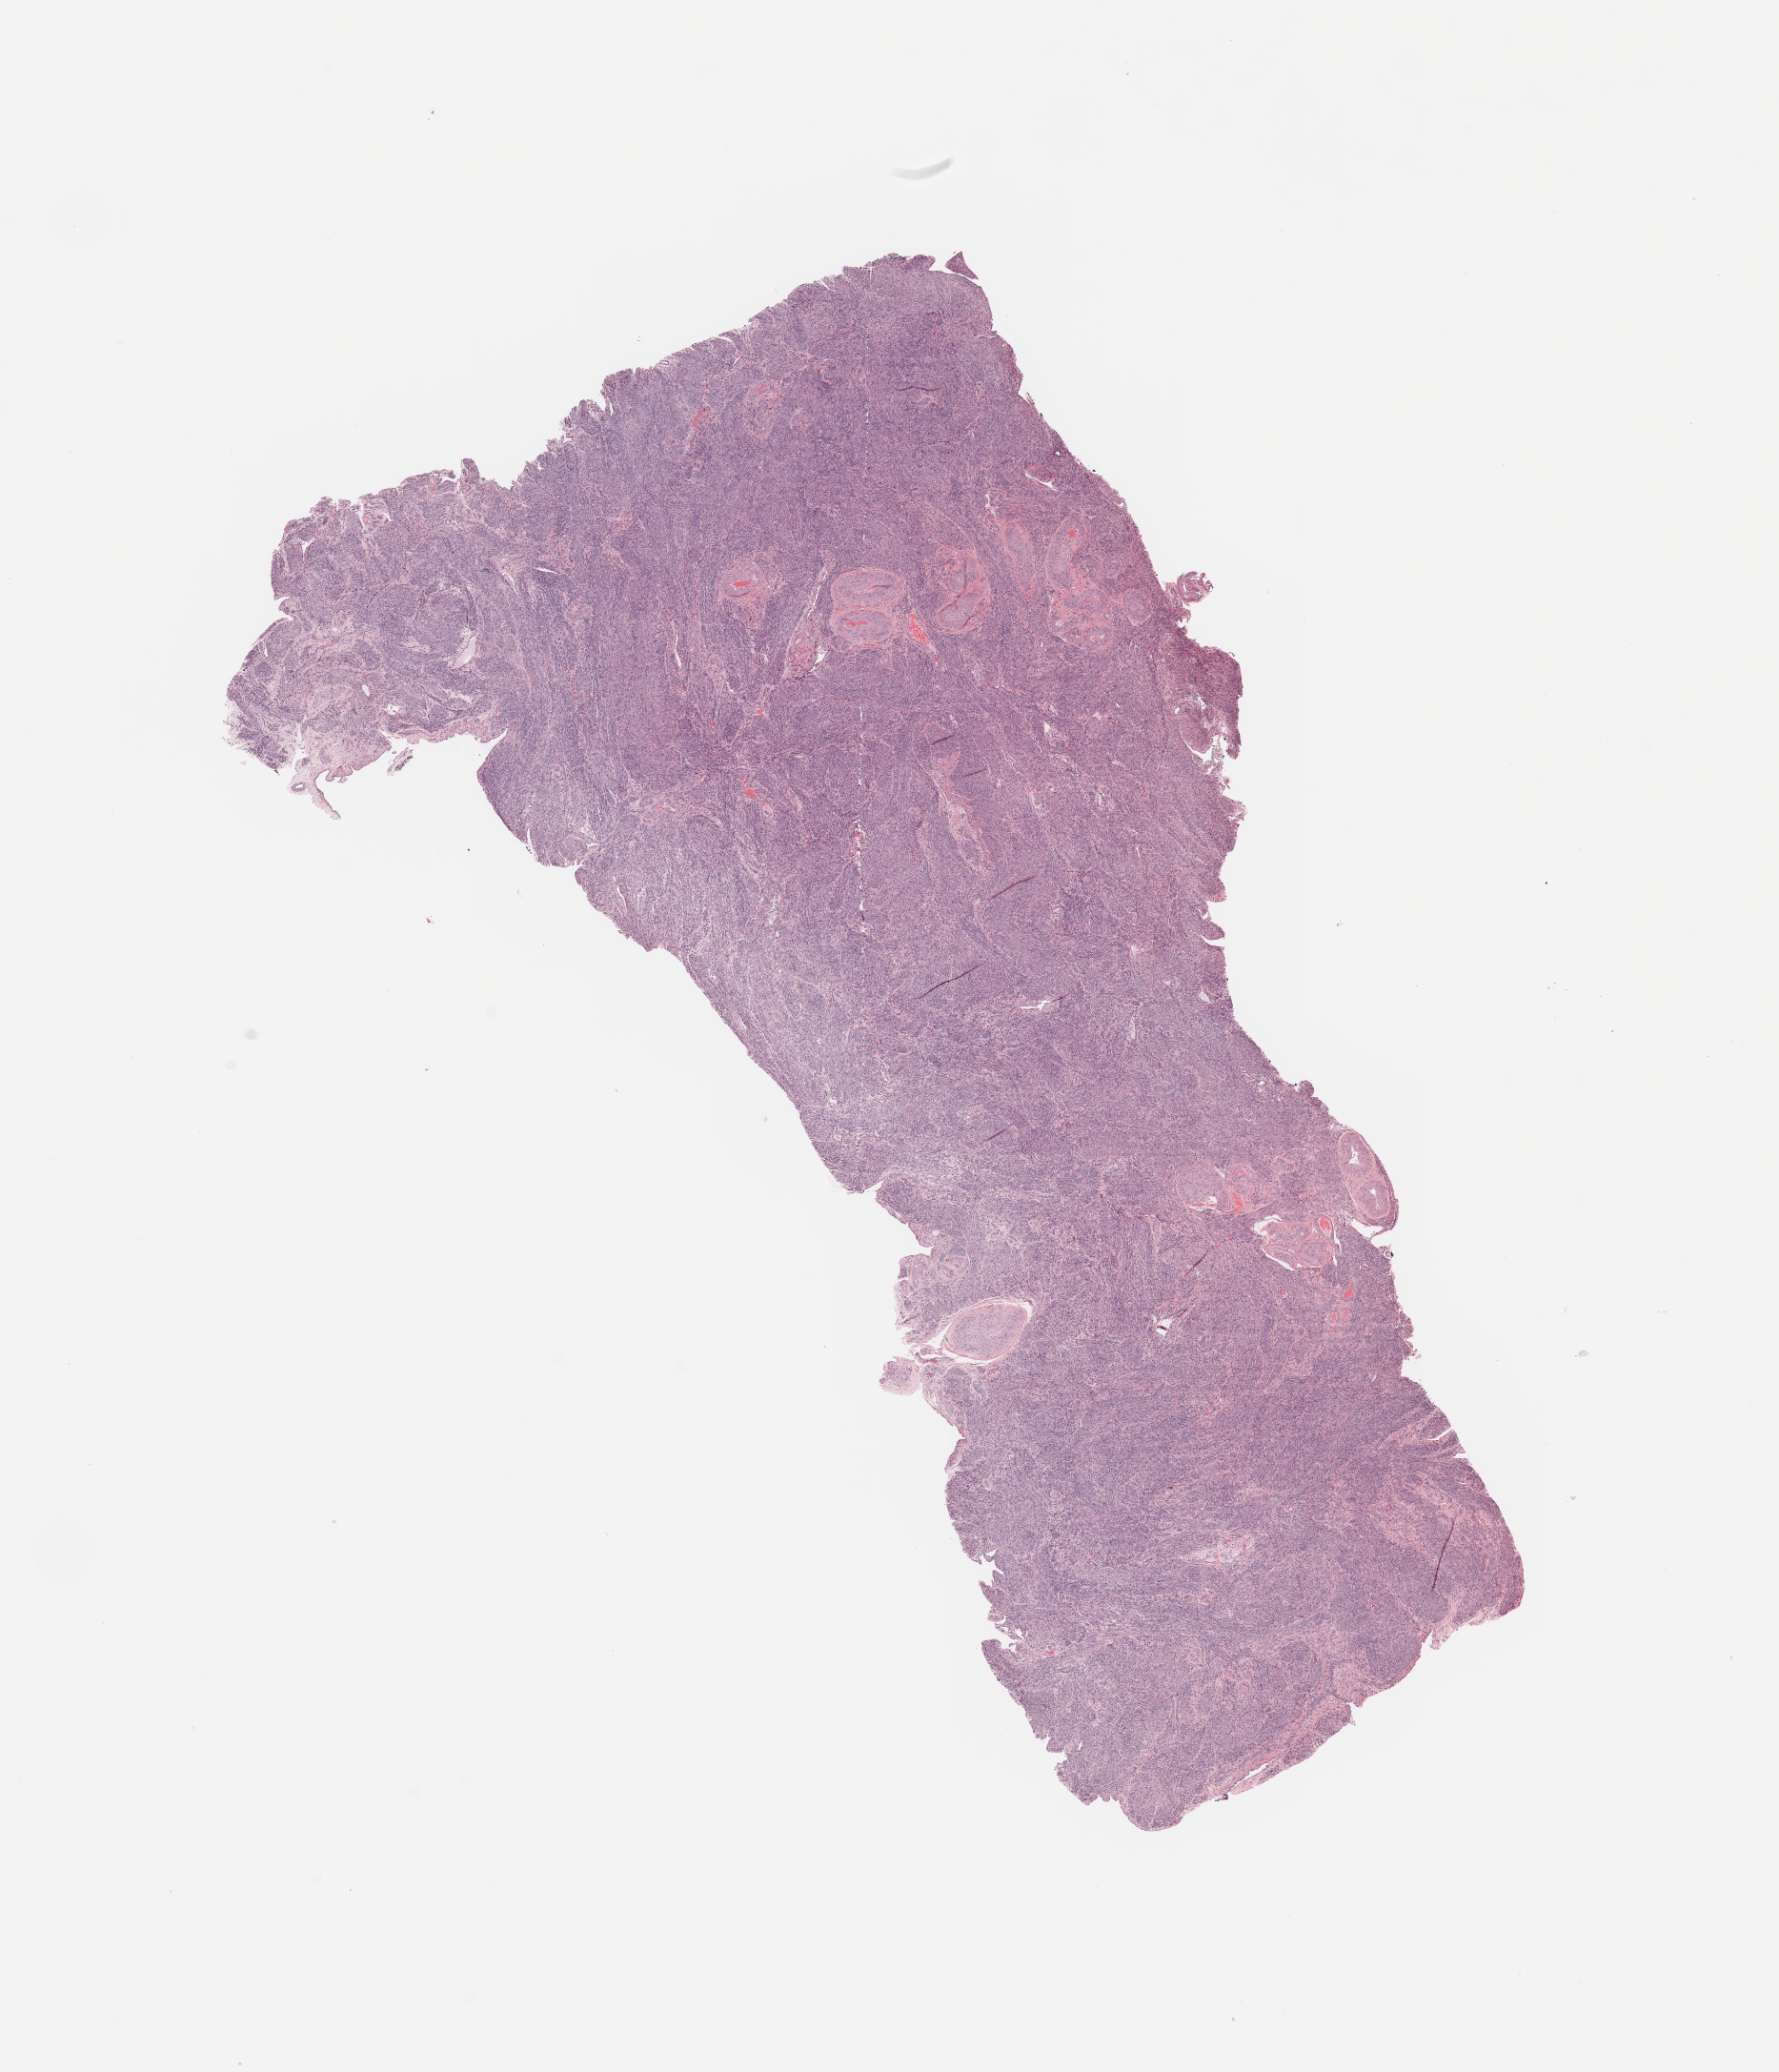
Whole-slide histology image, H&E-stained — whole scanned area (about 14.8 x 17.2 mm, from a 20x scan) shown as a low-resolution overview. Normal (non-tumour) tissue sample, sampled site: uterus. 61-year-old female patient.
- this section: normal (non-tumour) tissue from the same patient
- patient diagnosis: Endometrioid adenocarcinoma, NOS